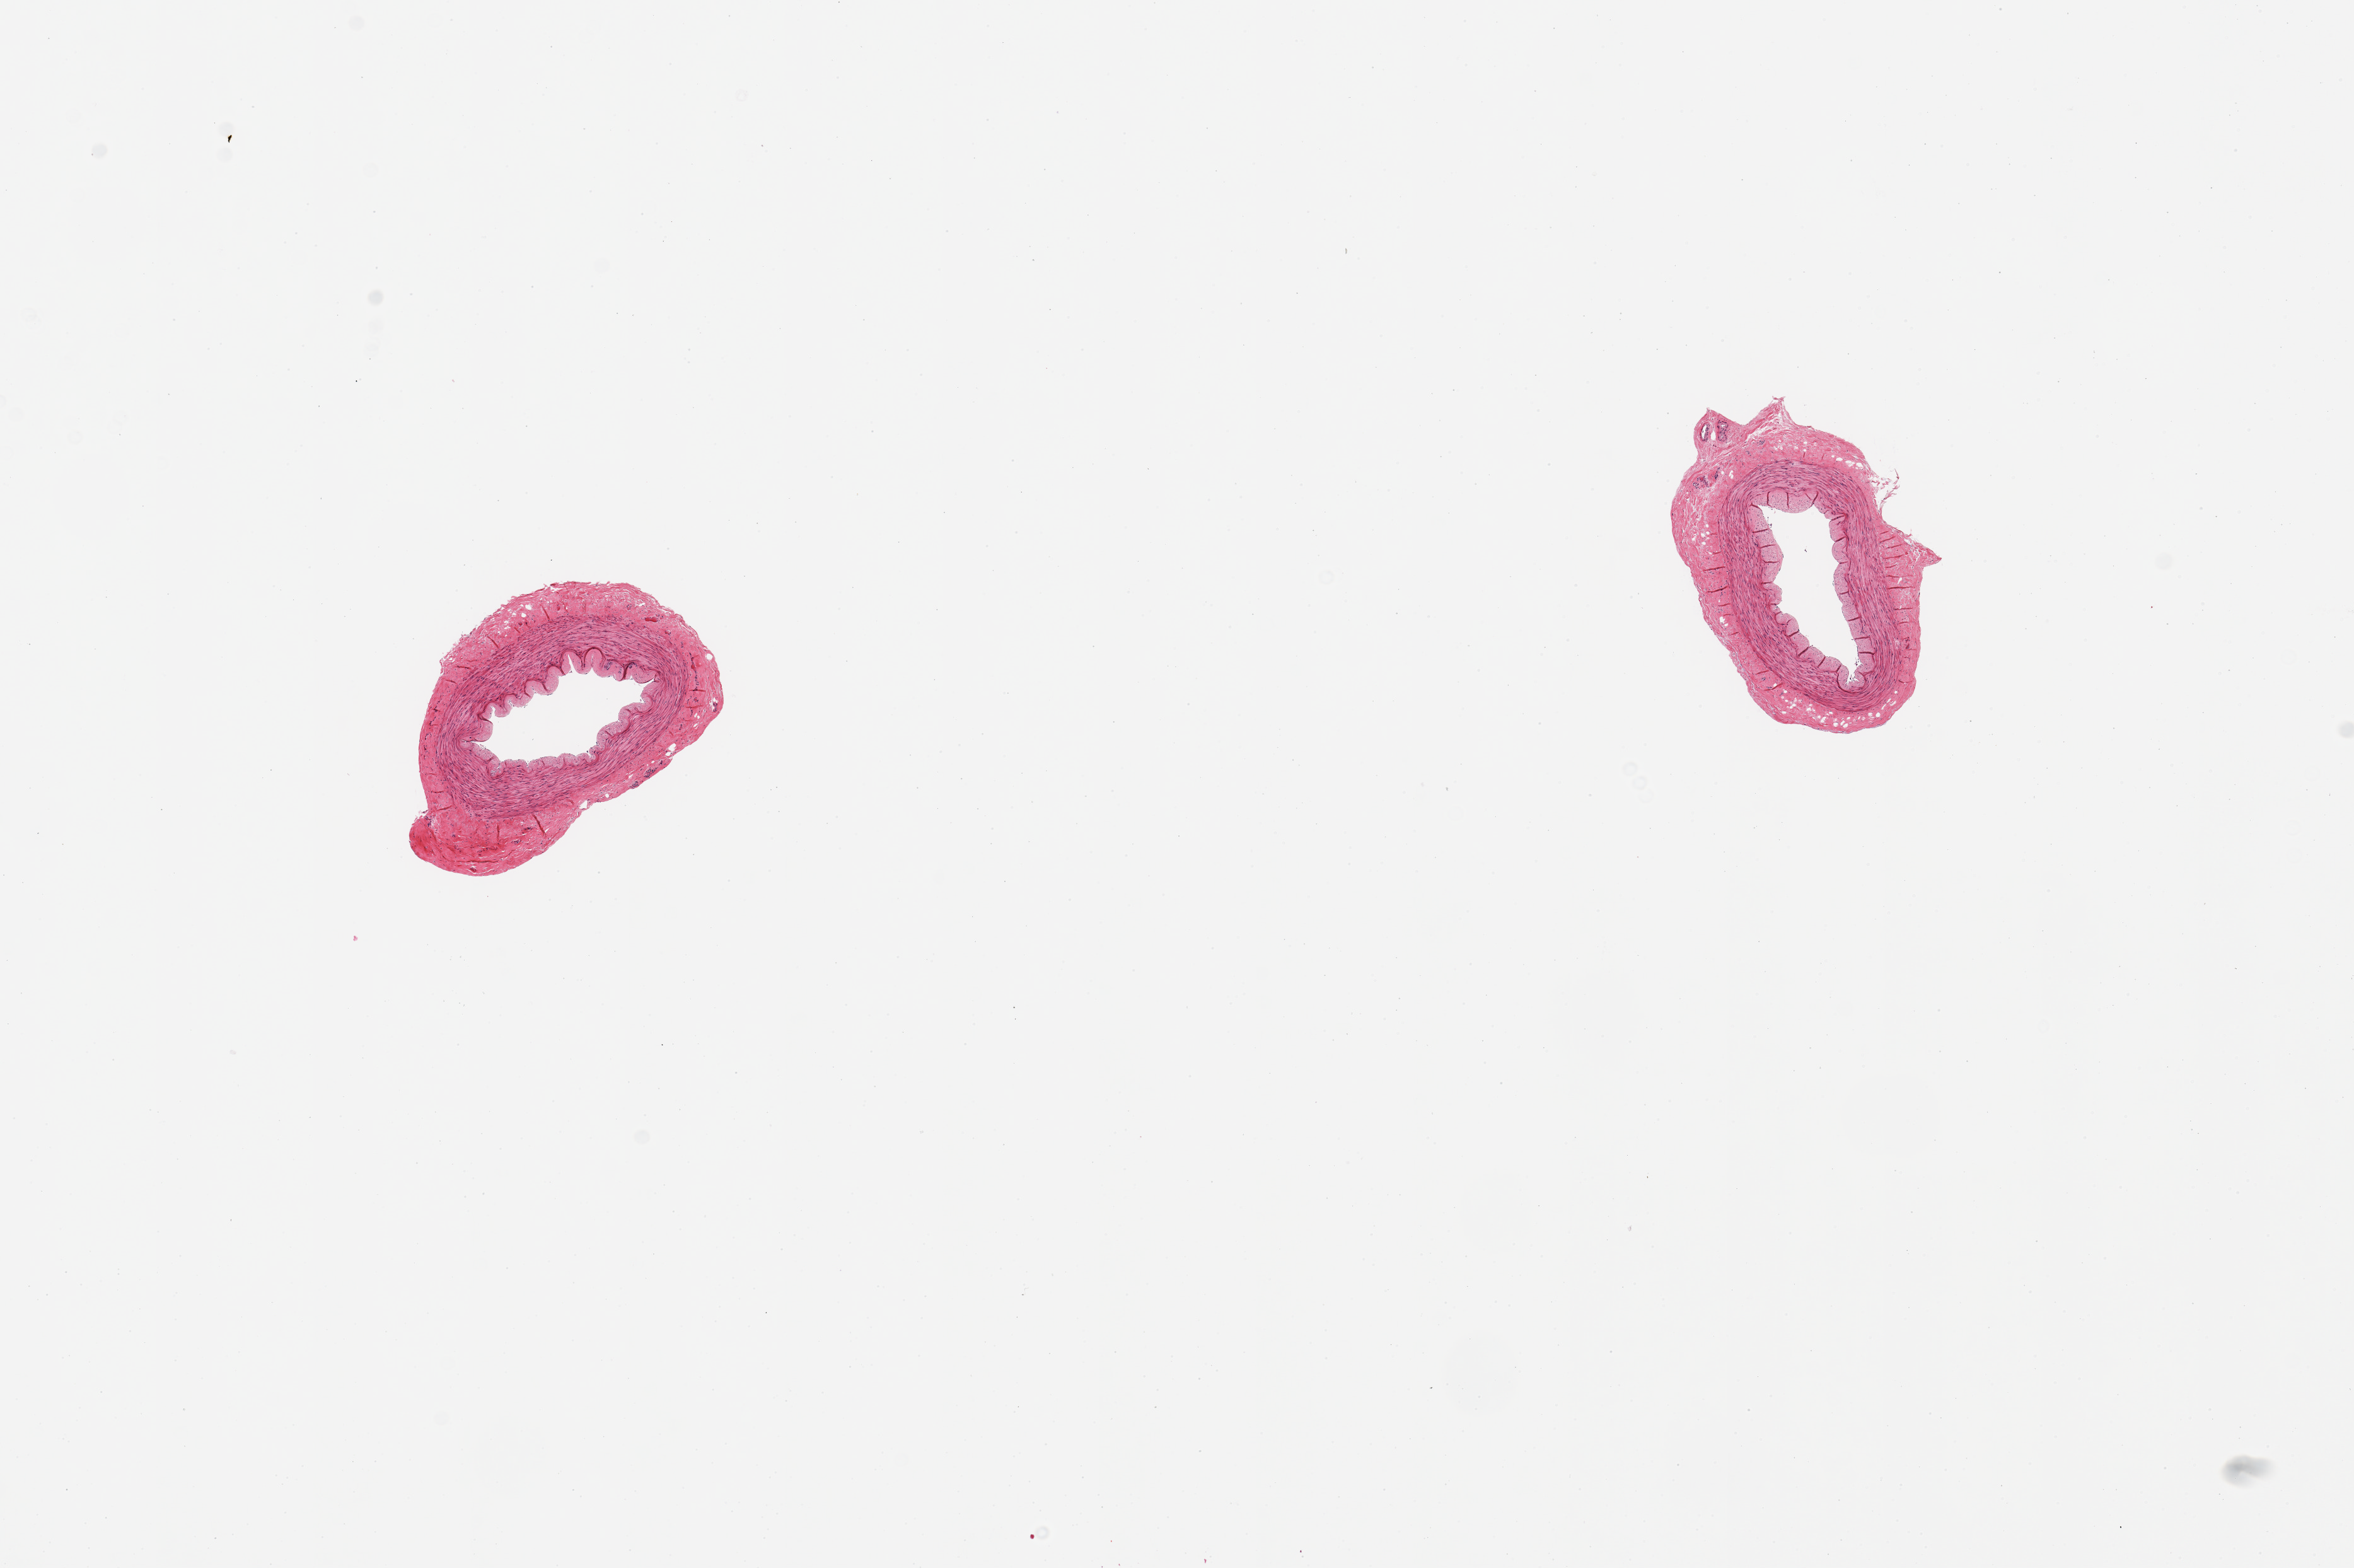
H&E whole-slide image — low-resolution overview of the scanned area, about 14.8 x 9.8 mm. PAXgene-fixed paraffin-embedded (PFPE) section. Section of tibial artery (target tissue). Donor tissue sample. Male donor.
- reviewer comment on this tissue sample: 2 pieces; no lesions; well trimmed